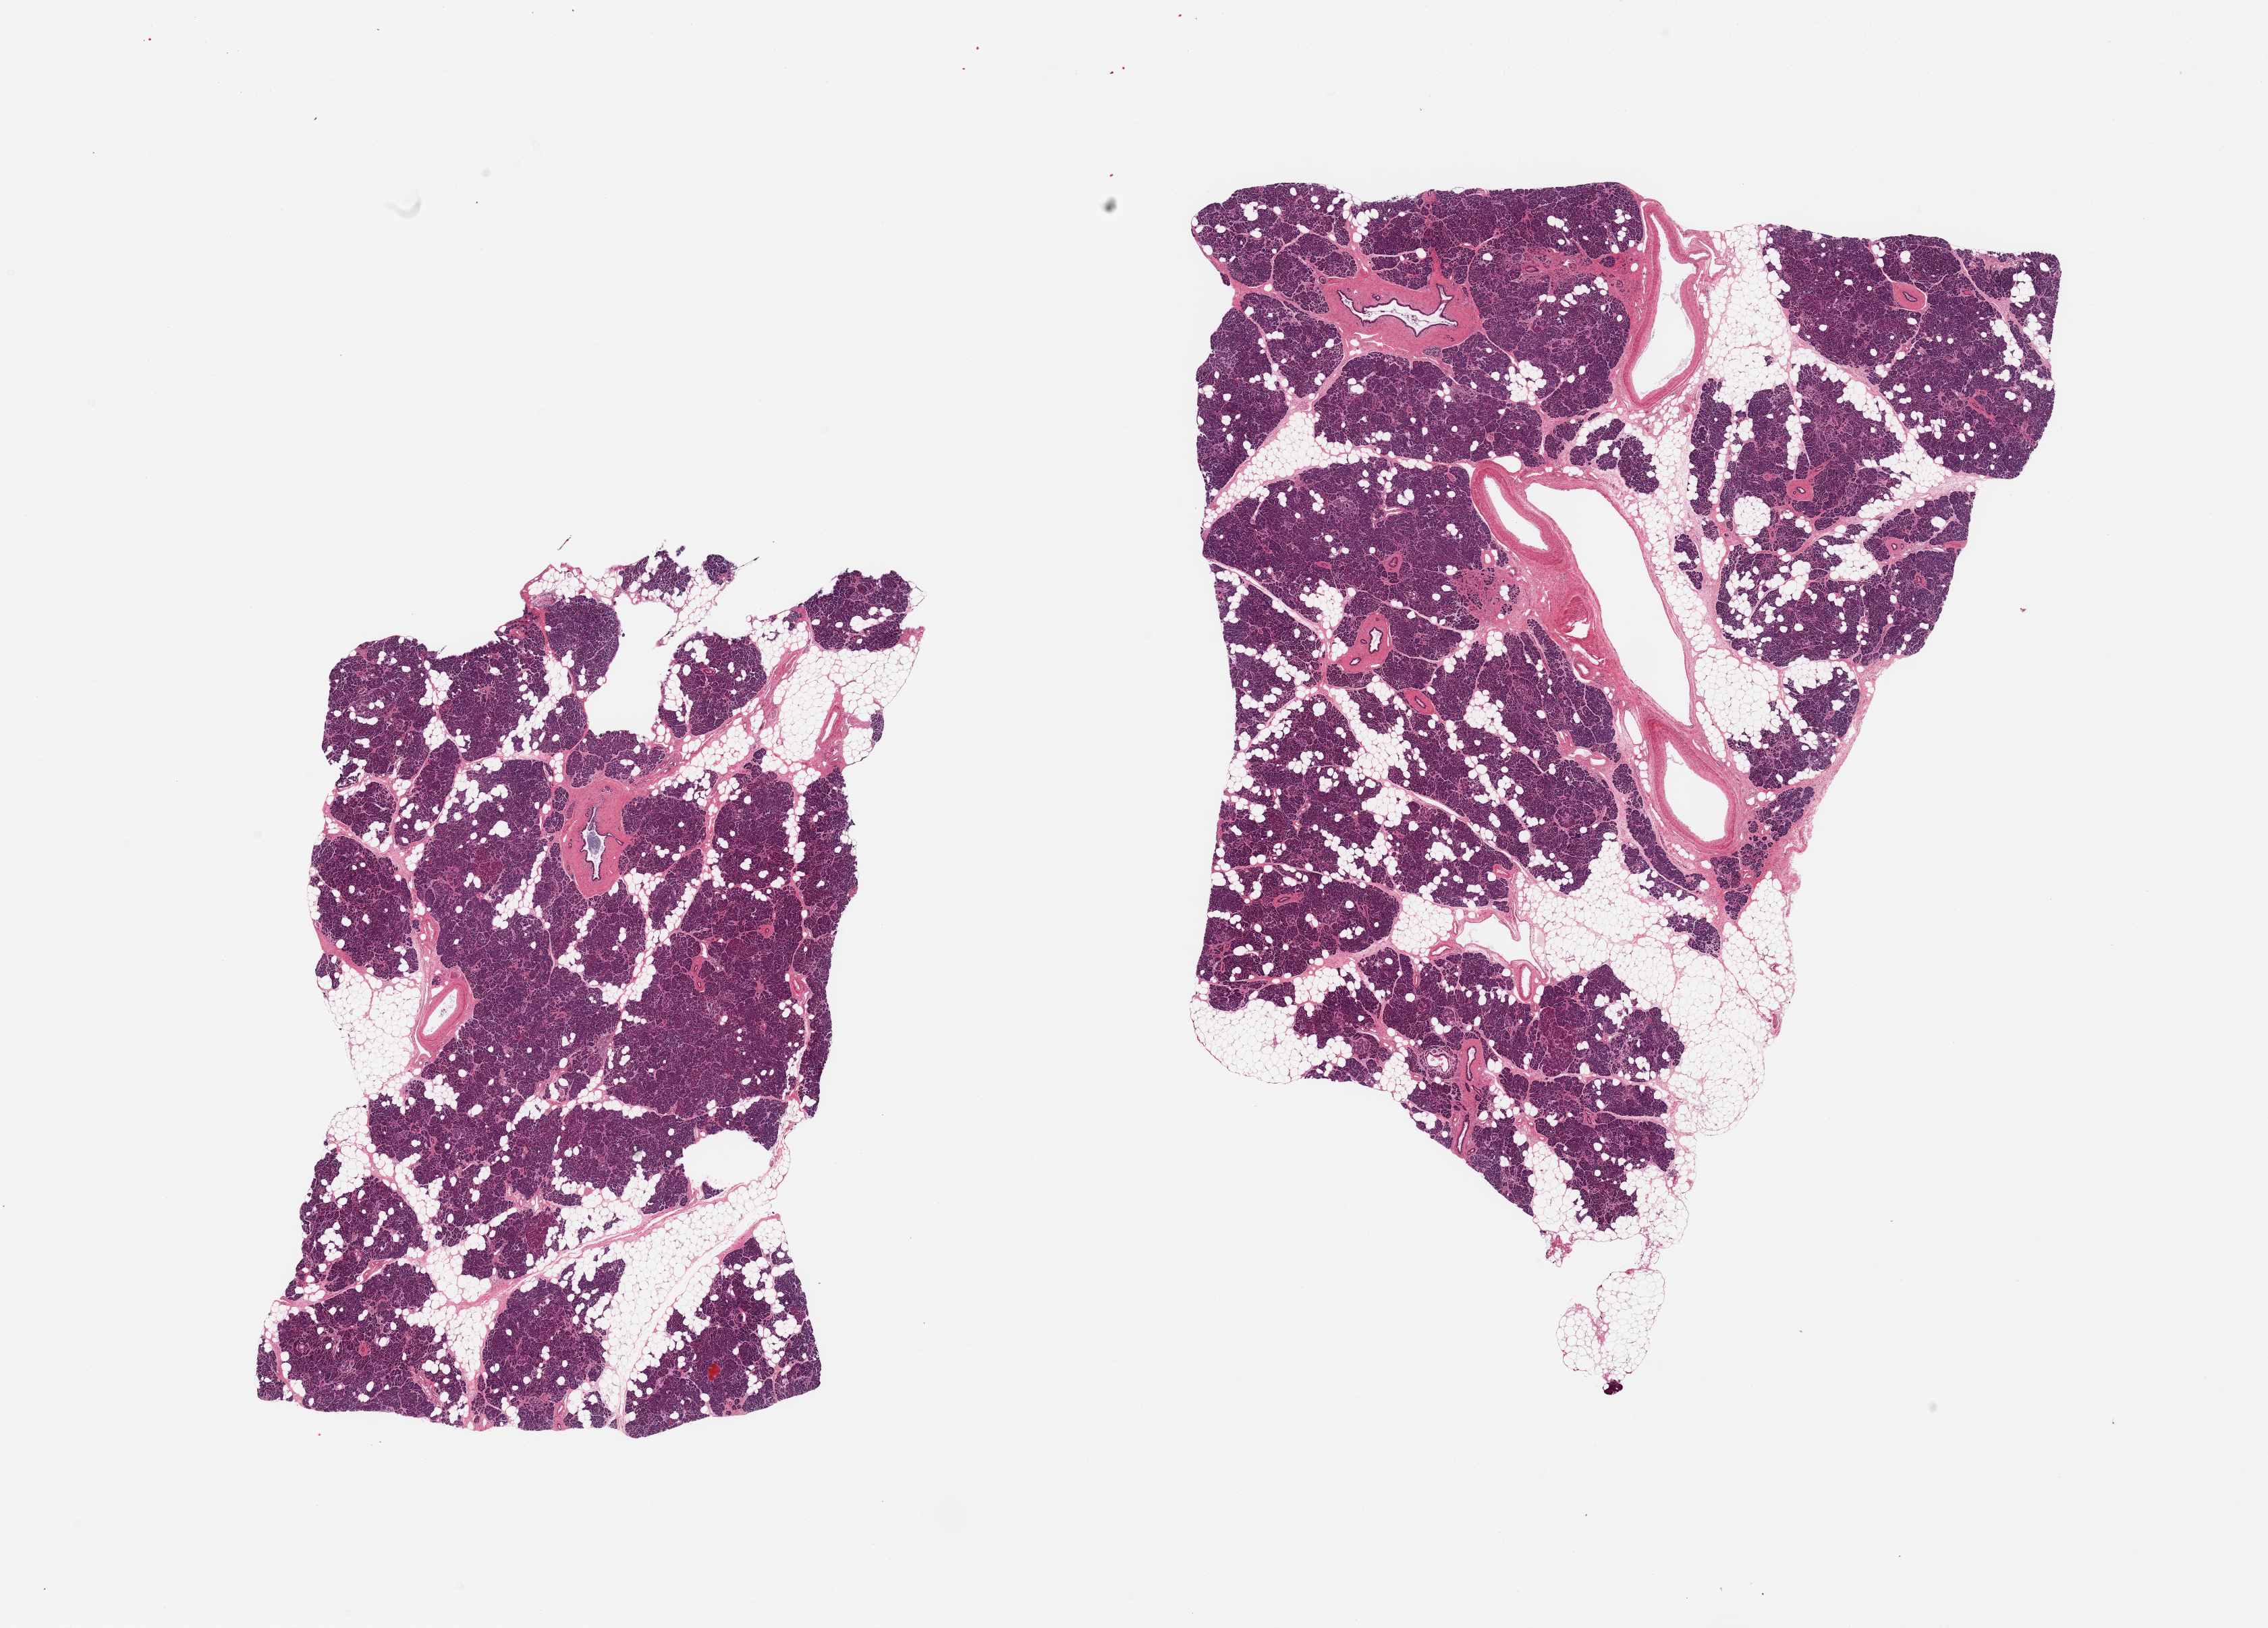
Whole-slide image, haematoxylin and eosin stain, whole scanned area (about 26.6 x 19.1 mm, slide scanned at 20x) shown as a low-resolution overview; PAXgene-fixed paraffin-embedded (PFPE) section; sampled site (target tissue): pancreas; tissue donor sample. Male donor.
* review note (as recorded): 2 pieces; both include ~30% attached and internal fat